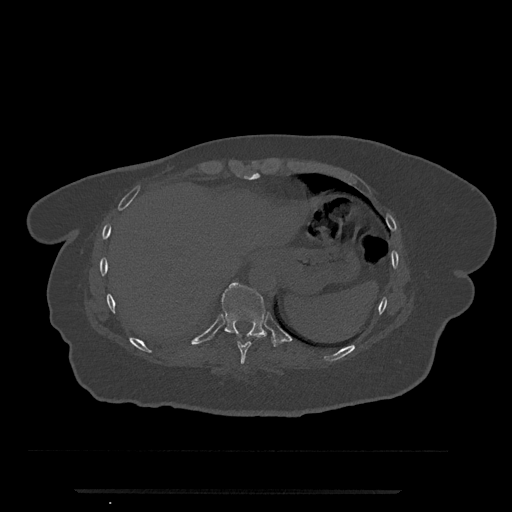
CT including the spine, one axial slice; 120 kVp; bone window (W 1800 / L 400 HU); 0.5 mm slice thickness; 512 × 512 image matrix, field of view 440 × 440 mm. Patient: female, 51 years. Case-level facts recorded for this patient, not image findings: primary cancer: neuro.
Outlined on this slice (semi-automatically segmented with operator editing):
- T10 vertebra: bounding box [x1, y1, x2, y2] px = [221, 282, 277, 346]
- T9 vertebra: [237, 337, 259, 365]